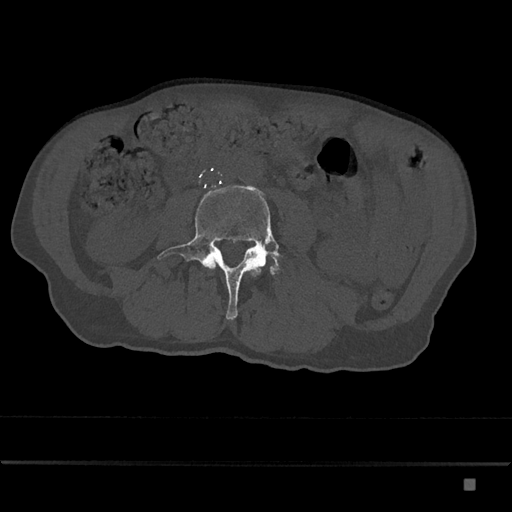
CT including the spine, one axial slice; position 345 of 797 along the scan axis; bone window (W 1800 / L 400 HU); 0.5 mm slice thickness; 512 × 512 image matrix, field of view 390 × 390 mm. Patient: male, 72 years. From the clinical record (not read from this slice): primary cancer: prostate.
Outlined on this slice (semi-automatic segmentation, software-assisted and operator-edited):
- L3 vertebra: box from (x=215, y=262) to (x=216, y=266) px
- L4 vertebra: (x=157, y=185)–(x=283, y=320)